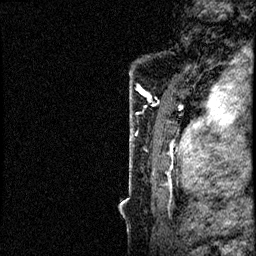
Breast MRI (dynamic contrast-enhanced), one sagittal slice; position 7 of 60 along the scan axis; dynamic contrast-enhanced study with each time point stored as its own series, time point 2 of 4 at this slice position (early post-contrast, ordered by acquisition time); 1.5 T; TE 4.2 ms, TR 17.6 ms; 2 mm slice thickness; 256 × 256 image matrix, field of view 200 × 200 mm. Female patient, age 40 years. From the clinical record (not read from this slice): setting: breast cancer imaged before/during neoadjuvant chemotherapy; receptor status: HER2-positive.
Structures marked on this image (semi-automatically segmented with operator editing):
- analysis volume of interest (the breast-tissue region the enhancement analysis was run in; not a lesion): box from (x=121, y=56) to (x=197, y=205) px
- tumour enhancement mask (voxels above the 100 % enhancement threshold inside the analysis volume of interest): (x=130, y=92)–(x=197, y=197)